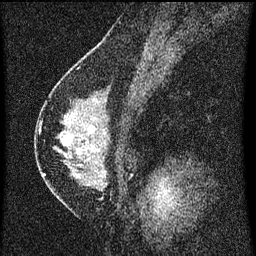
Breast MRI (dynamic contrast-enhanced), one sagittal slice; position 34 of 60 along the scan axis; dynamic contrast-enhanced series, image 2 of 3 at this slice position (ordered by acquisition); 1.5 T; TE 4.2 ms, TR 8 ms; 2 mm slice thickness; 256 × 256 image matrix, field of view 180 × 180 mm. Patient: female, 47 years.
Annotated regions visible in this slice (semi-automatically segmented with operator editing):
- analysis volume of interest (the breast-tissue region the enhancement analysis was run in; not a lesion): box from (x=42, y=92) to (x=138, y=199) px
- tumour enhancement mask (voxels above the 70 % enhancement threshold inside the analysis volume of interest): (x=44, y=132)–(x=106, y=177)